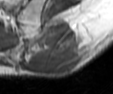
MRI of an extremity soft-tissue mass, one axial slice; MR volume resampled by the dataset authors to the PET/CT grid (not the native acquisition matrix); 3.27 mm slice thickness; 113 × 94 image matrix, field of view 110 × 92 mm. Male patient. From the clinical record (not read from this slice): histological type: leiomyosarcoma; grade: intermediate; site of the primary tumour: left pelvis.
Annotated regions visible in this slice (expert contour drawn on MRI and transferred to this co-registered scan by the dataset authors):
- gross tumour volume (mass): bounding box <22,20,82,74> (left, top, right, bottom; pixels)